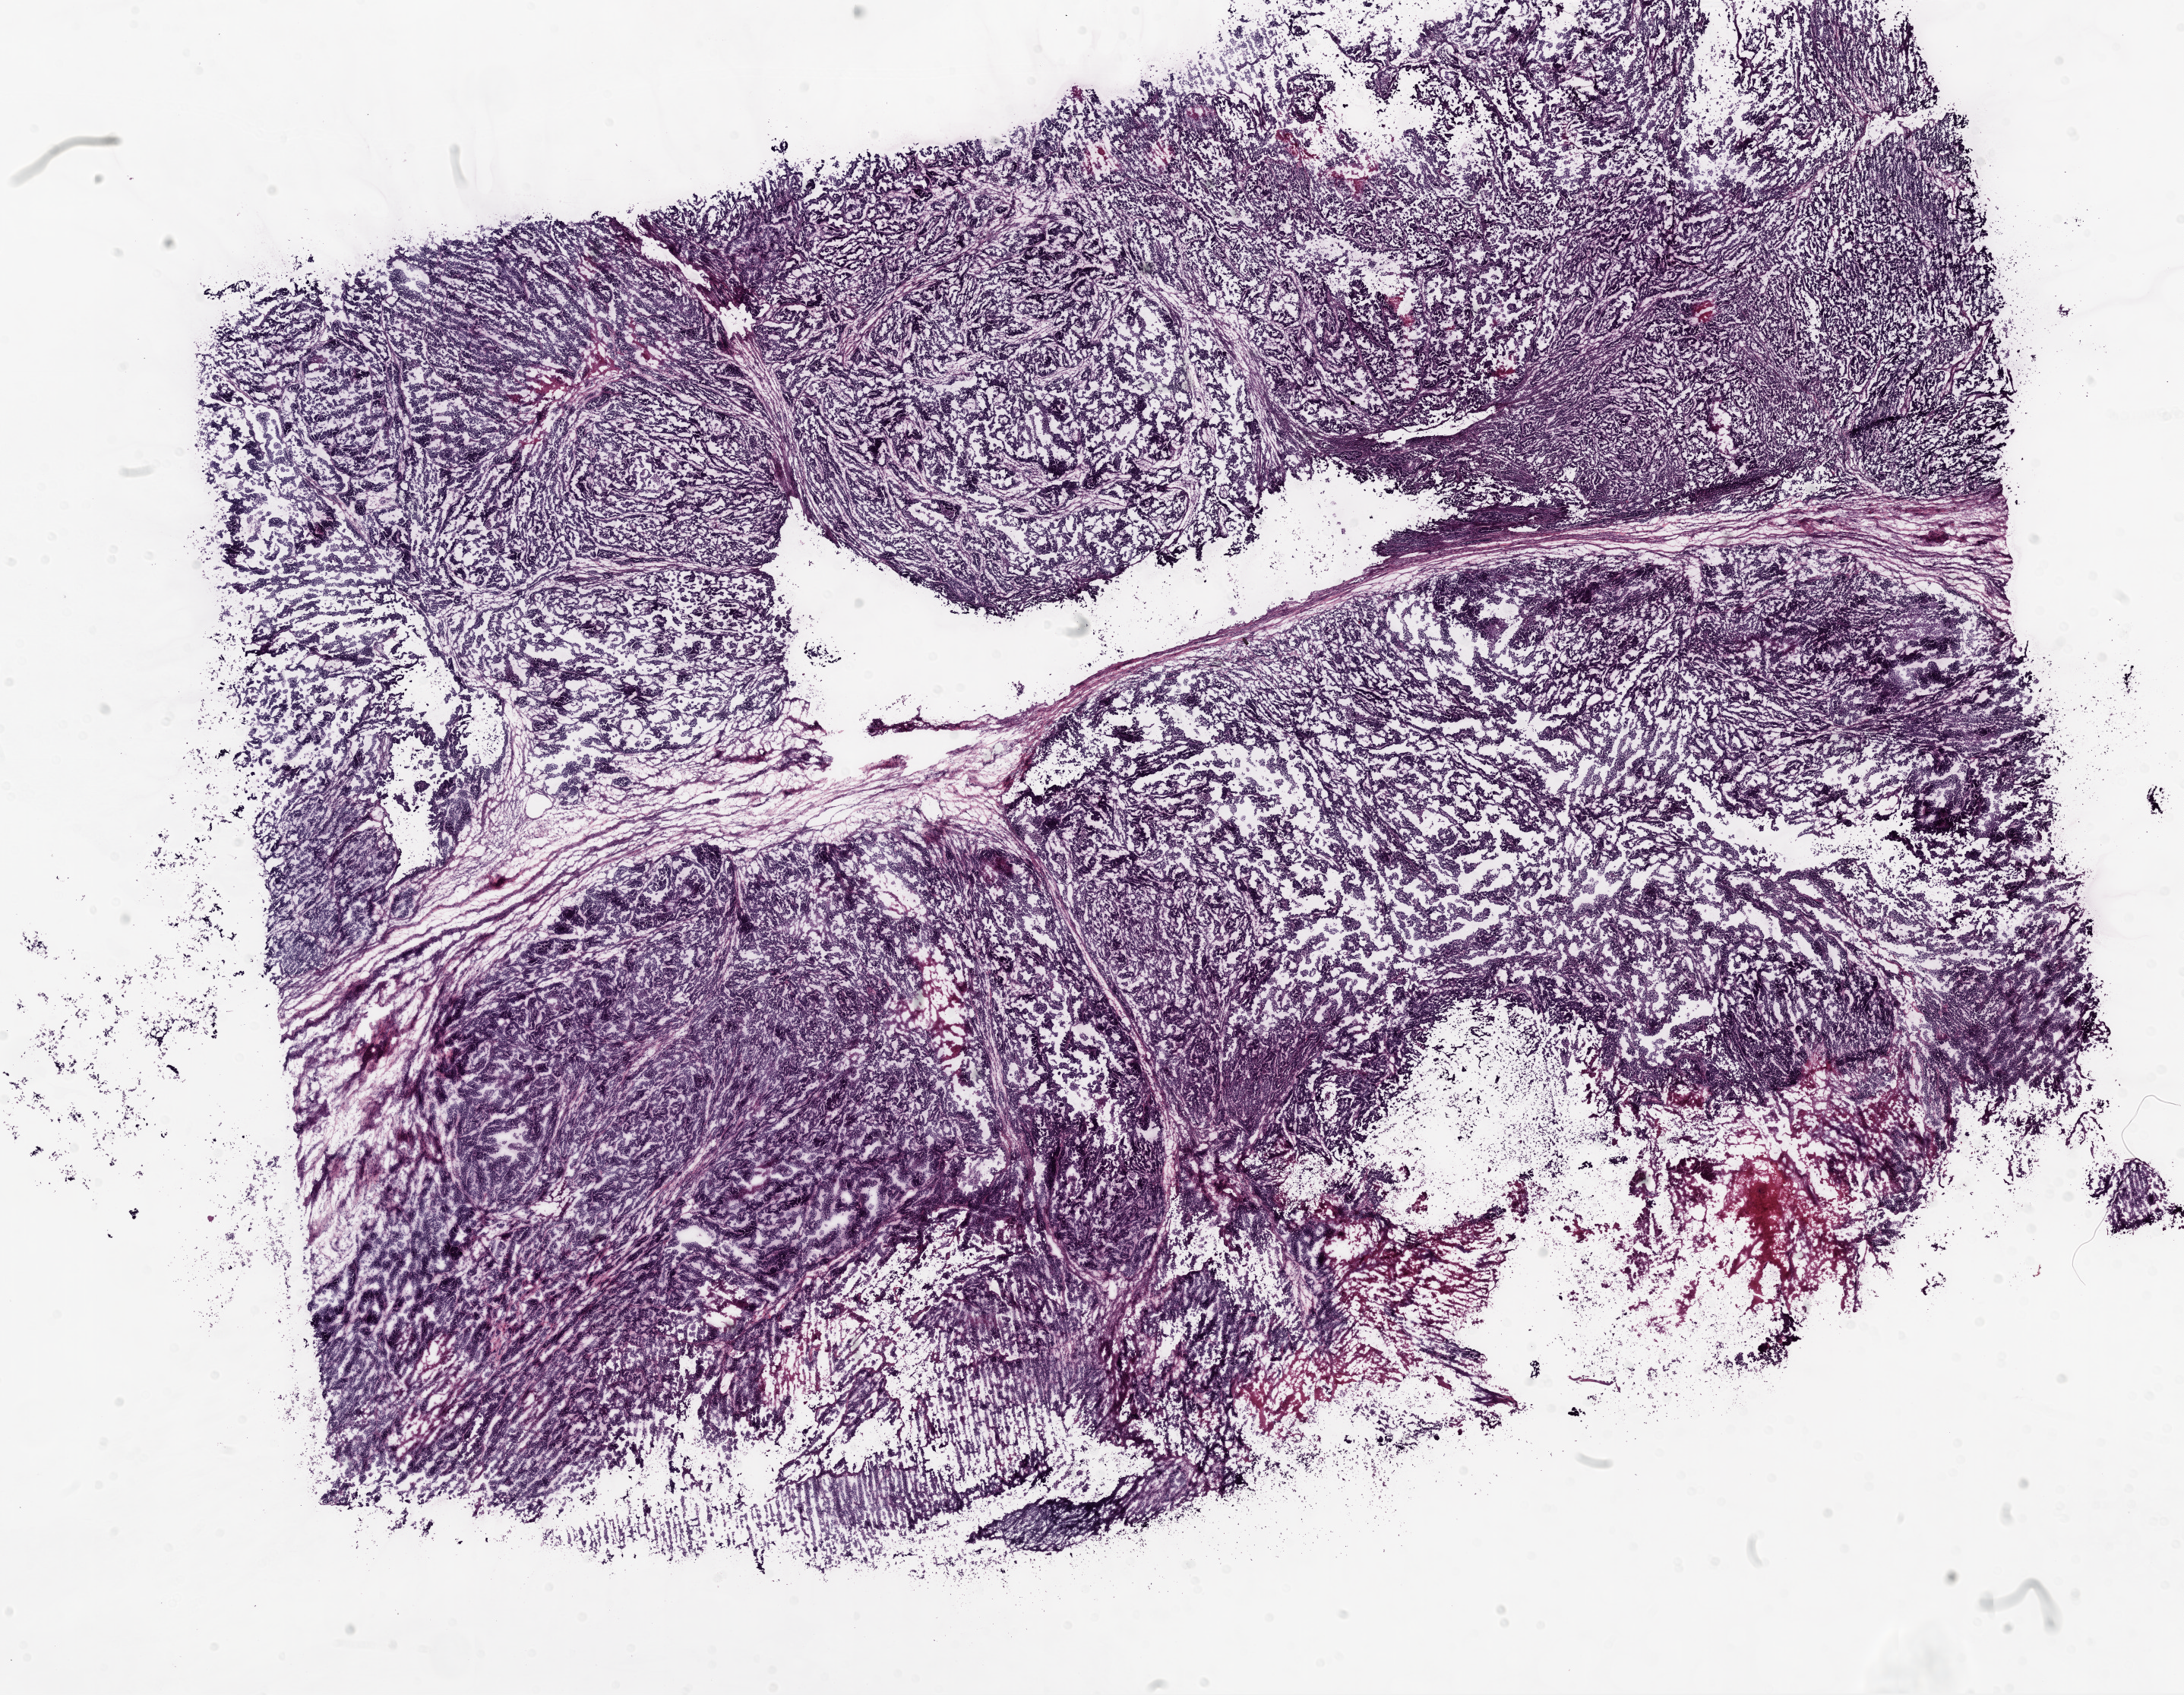
Digitized Hematoxylin and eosin (H&E) stained tissue section (whole slide) — whole scanned area (about 23.1 x 17.9 mm) shown as a low-resolution overview, frozen section from the top of the tissue portion, ovary, primary tumour sample. Female patient; age at initial diagnosis 58 years.
Histologic diagnosis: Serous cystadenocarcinoma, NOS.